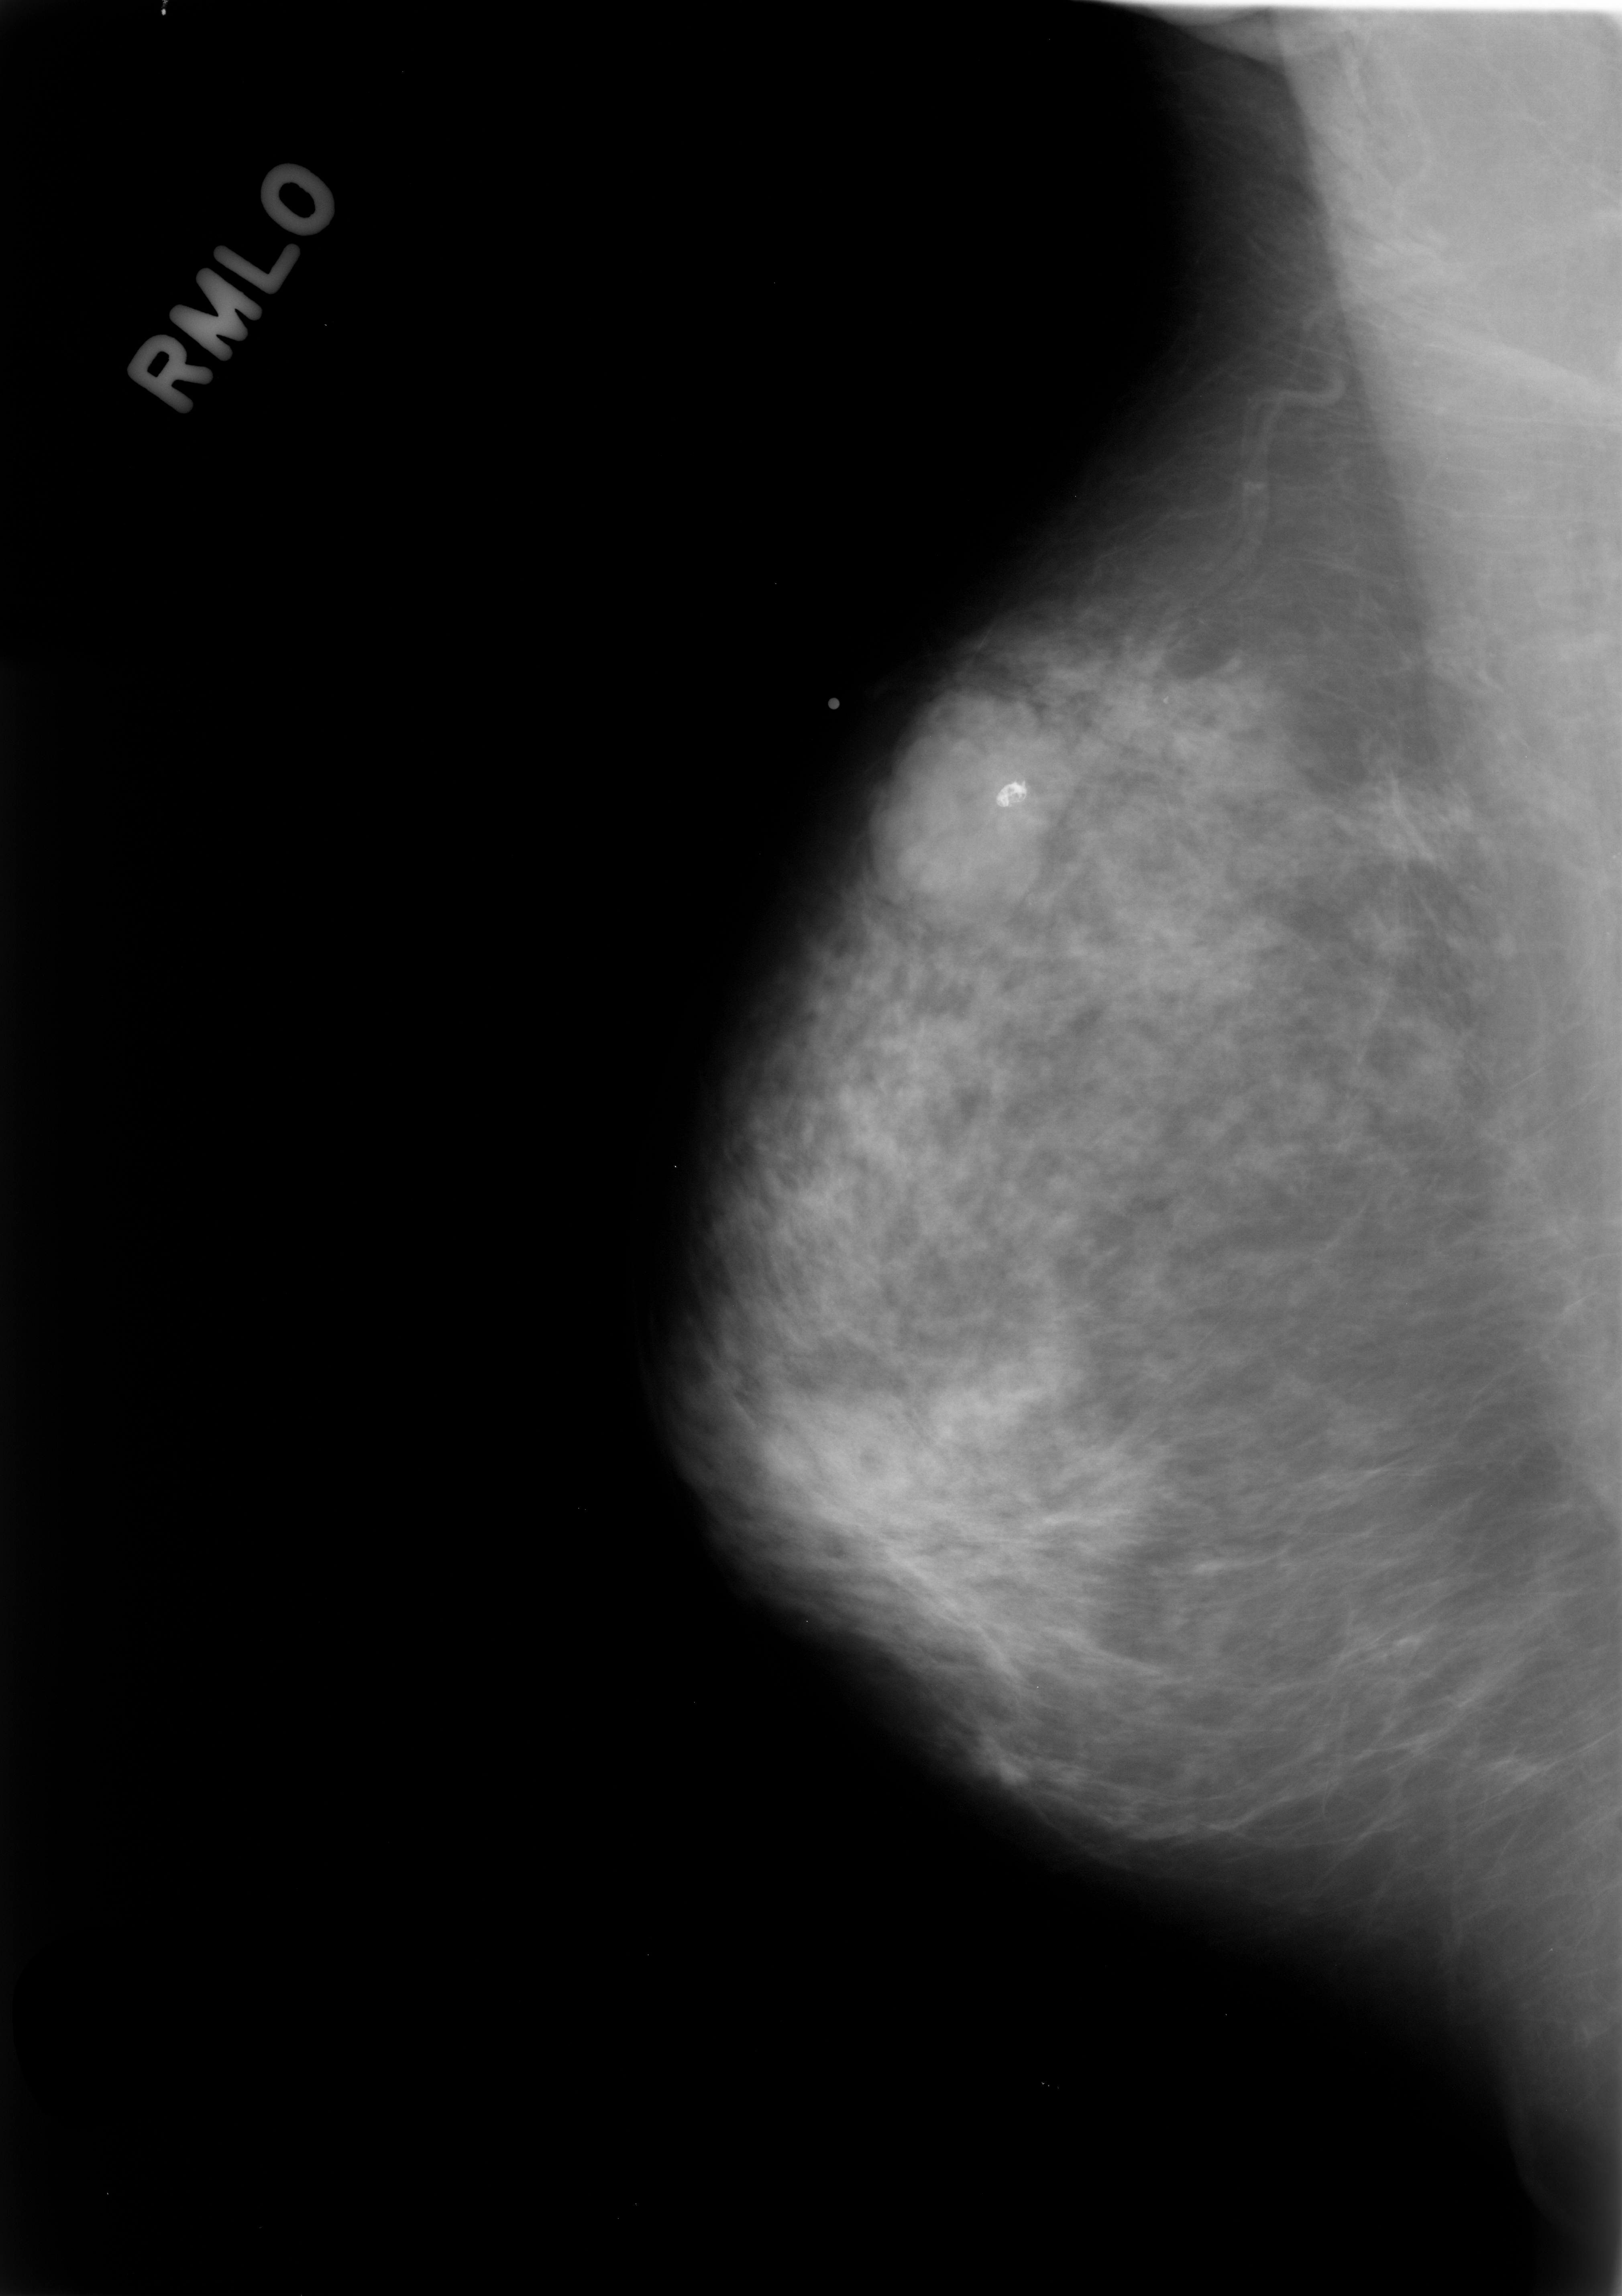
Scanned film-screen mammogram; right breast; mediolateral oblique (MLO) view; BI-RADS breast density category 2 (scale 1–4).
Radiologist-marked abnormalities on this image: mass, shape lobulated, margins microlobulated; BI-RADS assessment category 4; subtlety rating 5 on a 1 (subtle) to 5 (obvious) scale; pathology (as recorded): benign.